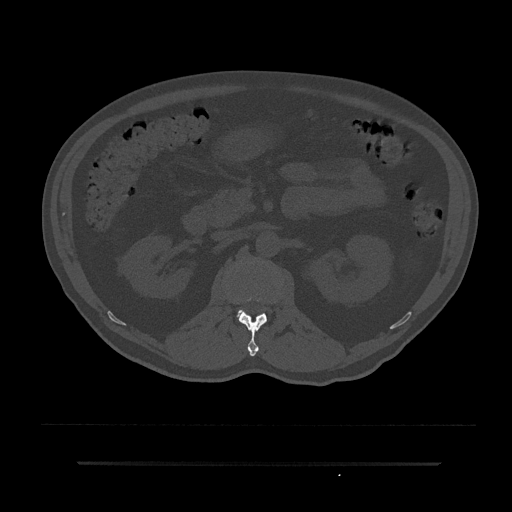
CT including the spine, one axial slice; slice 117 of 797 in the series (ordered by position); 120 kVp; bone window (W 1800 / L 400 HU); 0.5 mm slice thickness; 512 × 512 image matrix. Patient: male, 59 years. Case-level facts recorded for this patient, not image findings: primary cancer: bile ducts.
Annotated regions visible in this slice (semi-automatic segmentation, software-assisted and operator-edited):
- L1 vertebra: bounding box (x1, y1, x2, y2) in pixels: (239, 297, 267, 356)
- L2 vertebra: (238, 309, 244, 319)